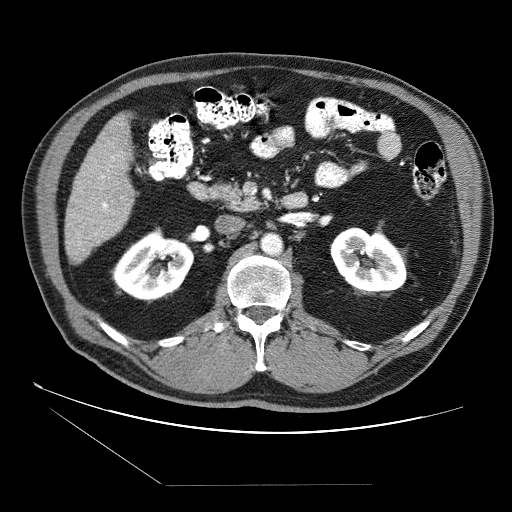
Contrast-enhanced abdominal CT (liver protocol), one axial slice; slice 19 of 87 in the series (ordered by position); reconstruction kernel STANDARD; soft-tissue window (W 400 / L 40 HU); 2.5 mm slice thickness; 512 × 512 image matrix. From the clinical record (not read from this slice): diagnosis: hepatocellular carcinoma (patient treated with transarterial chemoembolisation; whether this scan precedes or follows treatment is not stated here); TNM stage (as recorded): Stage-II; Child-Pugh class: B.
Structures marked on this image (semi-automatic segmentation, software-assisted and operator-edited):
- liver parenchyma outside the tumour (the mass and vessels are separate outlines, so this box may not span the whole liver): bounding box [x1, y1, x2, y2] px = [64, 114, 134, 264]
- liver vessels: [78, 154, 121, 245]